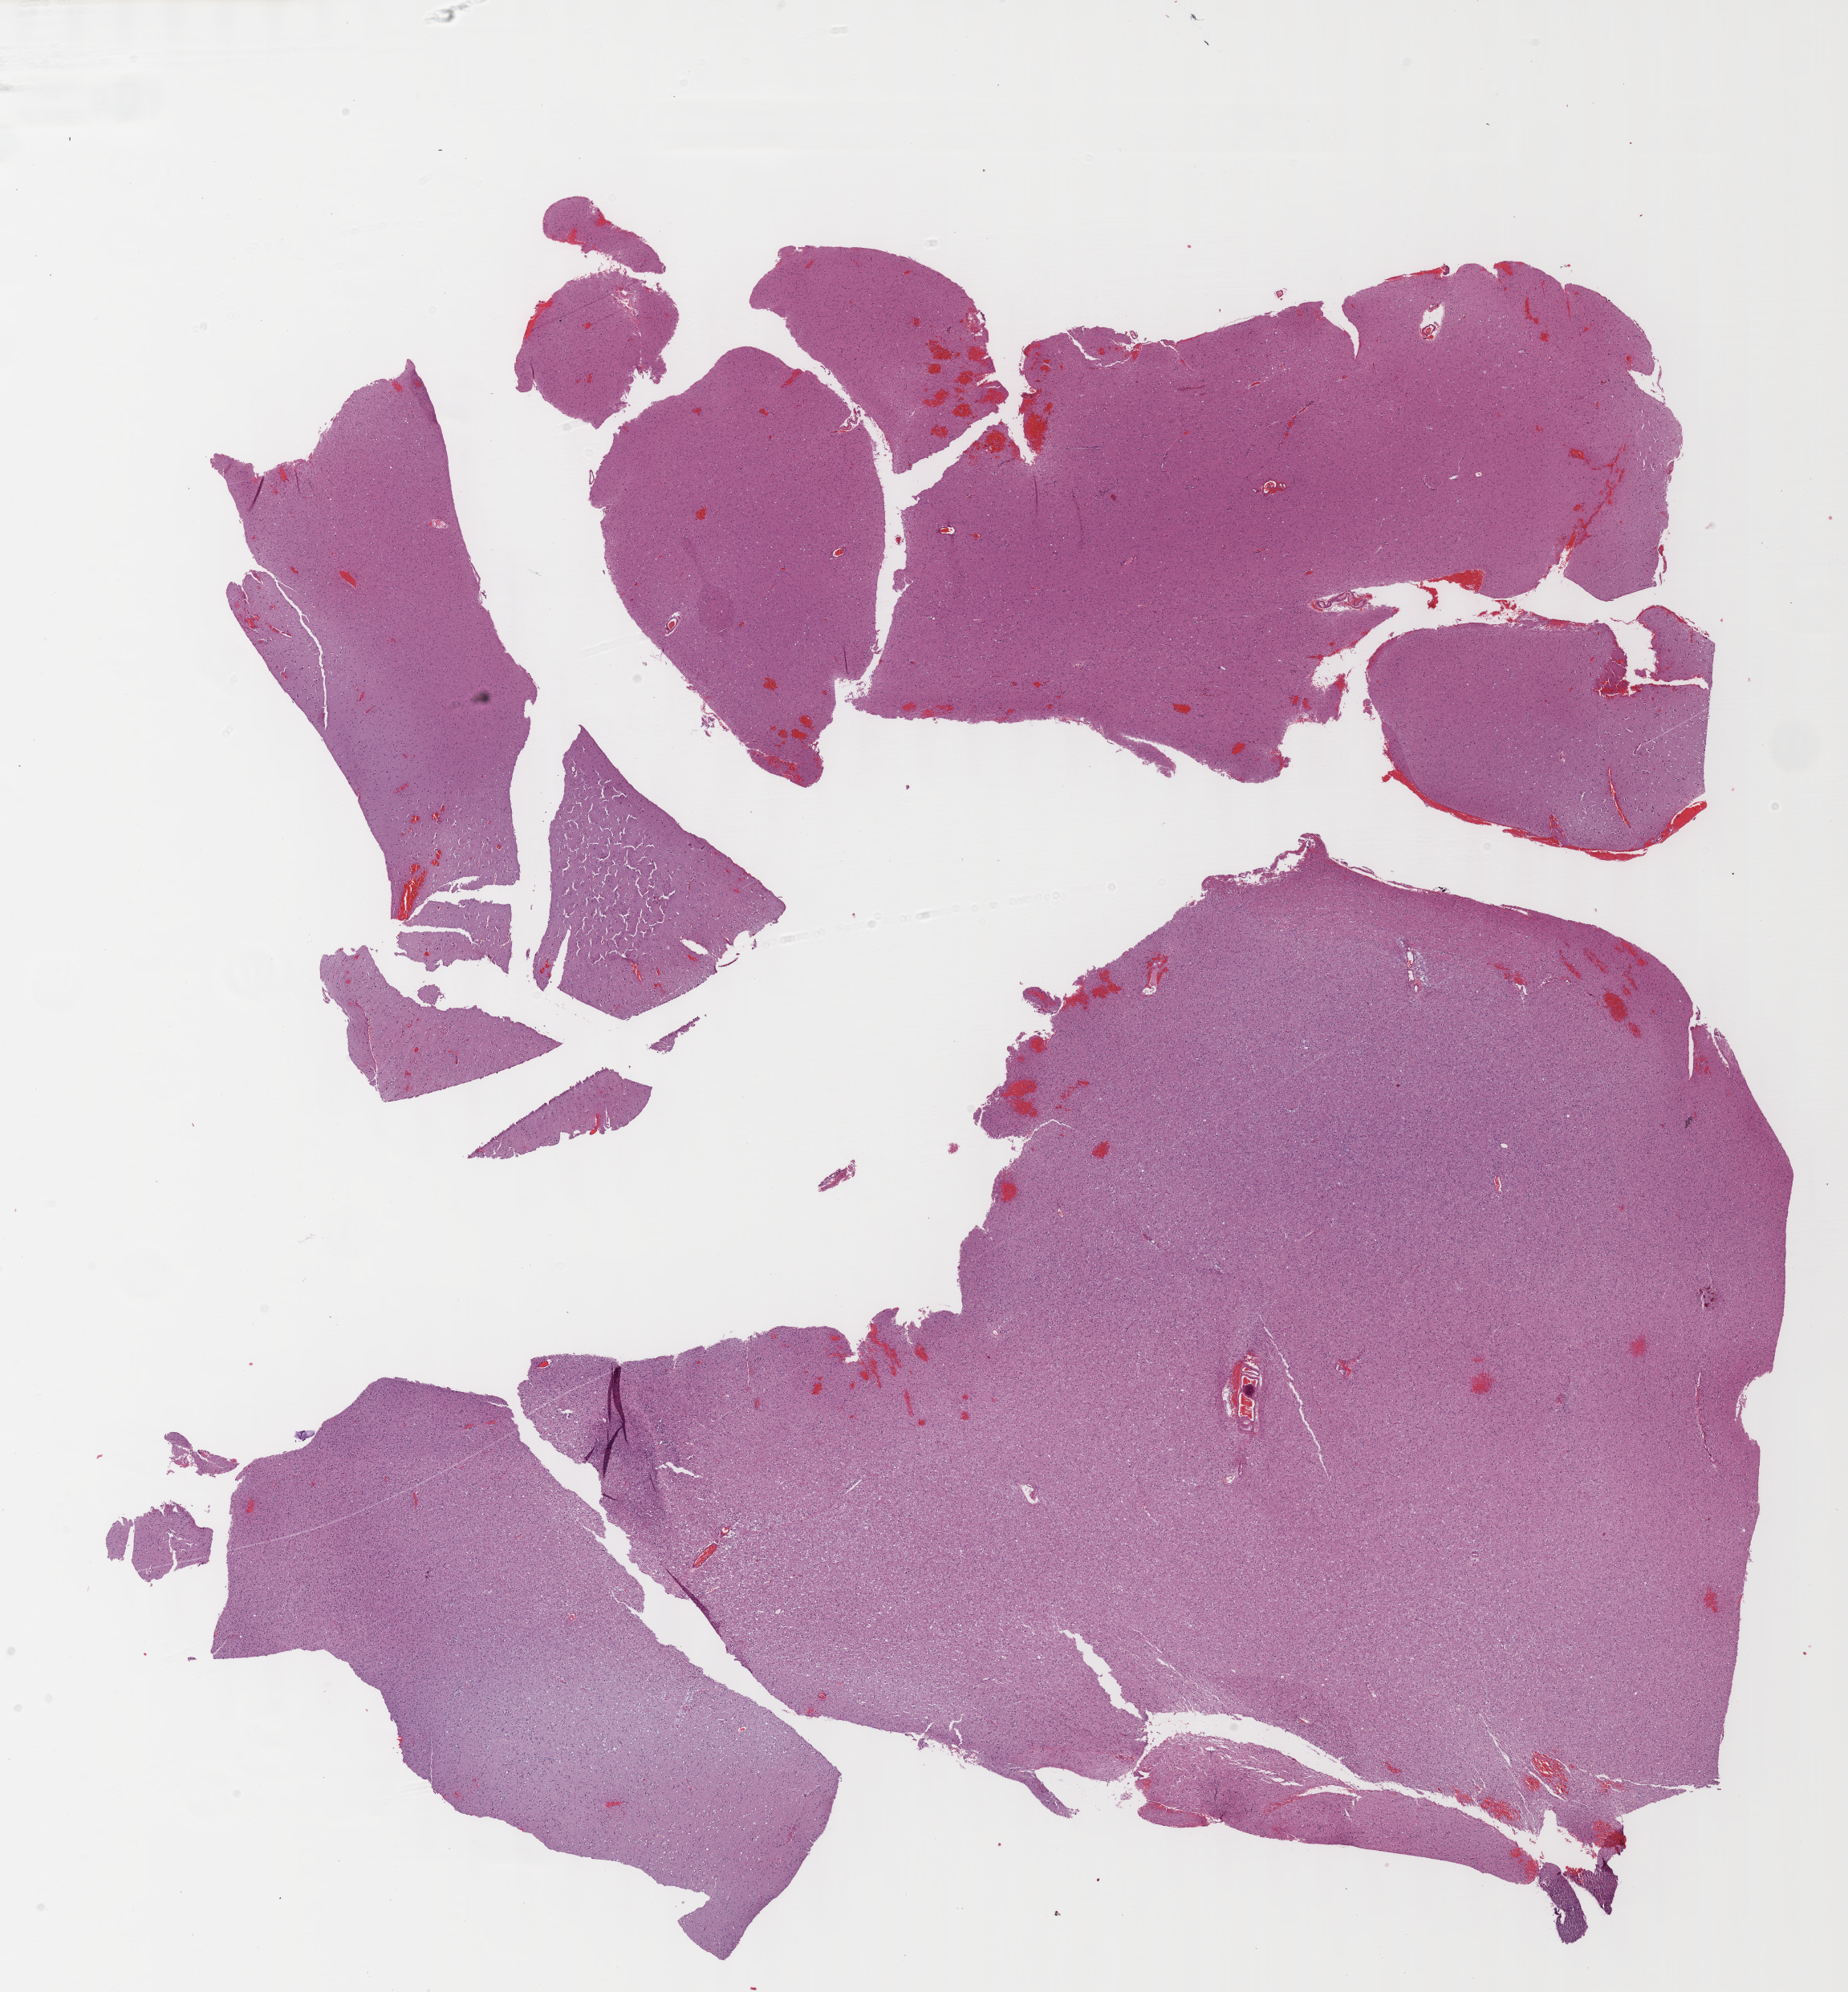
H&E-stained whole-slide image, shown as a low-resolution overview of the whole scanned area (about 18.6 x 20.1 mm, from a 40x scan); formalin-fixed paraffin-embedded (FFPE) diagnostic section; primary tumour sample from the brain. Female patient; age at initial diagnosis 29 years. Histologic grade: G2 (moderately differentiated).
- histologic diagnosis: Oligodendroglioma, NOS (cerebrum)